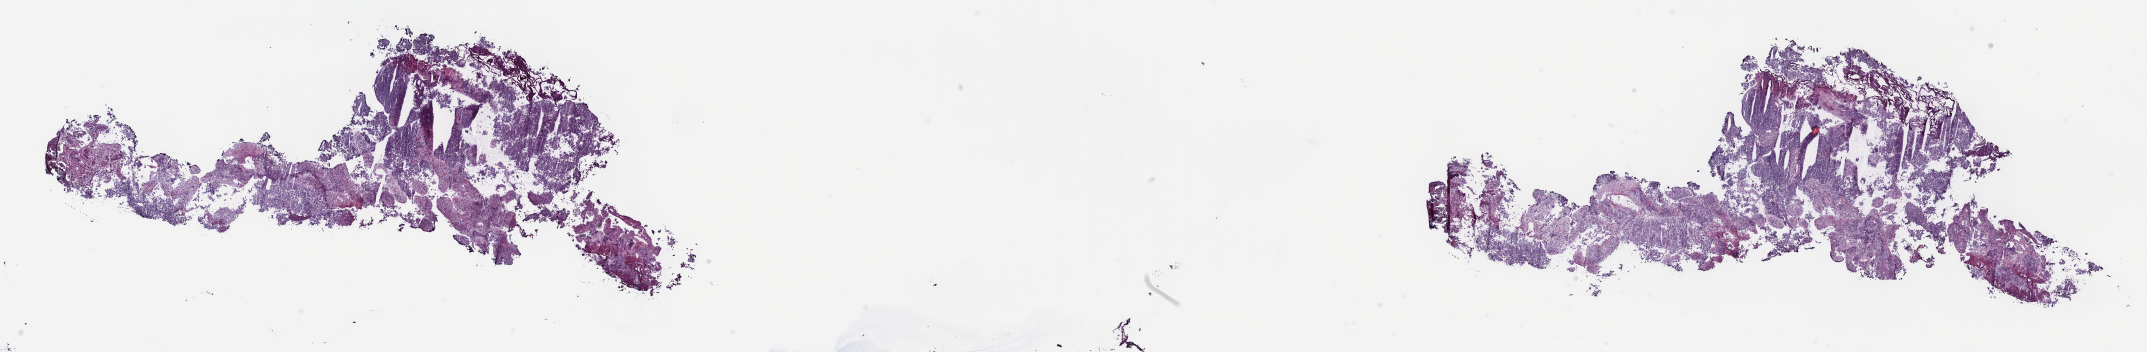
Digitized H&E tissue section (whole slide) — whole scanned area (about 34.7 x 5.7 mm) shown as a low-resolution overview; frozen section from the top of the tissue portion; sample: primary tumour, bladder. Male, age 78 years at initial diagnosis. Histologic grade: high grade. Pathologist review of this section (percent, as recorded): tumour cells 100%, tumour nuclei 65%, normal cells 0%, stromal cells 0%, necrosis 0%. Infiltration values recorded for this section: lymphocyte infiltration 2%, monocyte infiltration 0%, neutrophil infiltration 0%.
• AJCC pathologic stage: II (7th edition)
• histologic diagnosis: Transitional cell carcinoma